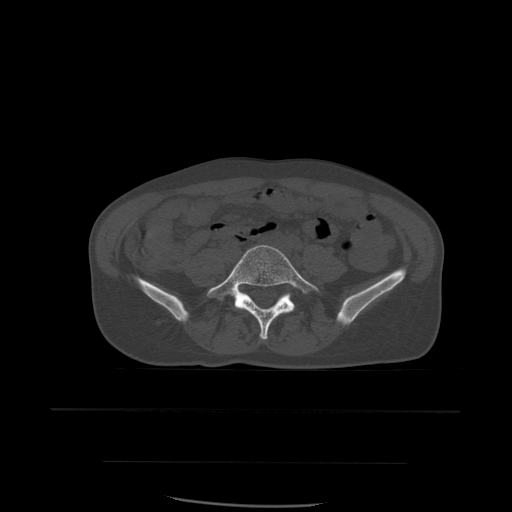
CT including the spine, one axial slice; bone window (W 1800 / L 400 HU); 512 × 512 image matrix. Patient age 48 years. Case-level facts recorded for this patient, not image findings: primary cancer: lung.
Outlined on this slice (semi-automatically segmented with operator editing):
- L5 vertebra: bounding box [x1, y1, x2, y2] px = [207, 245, 321, 340]